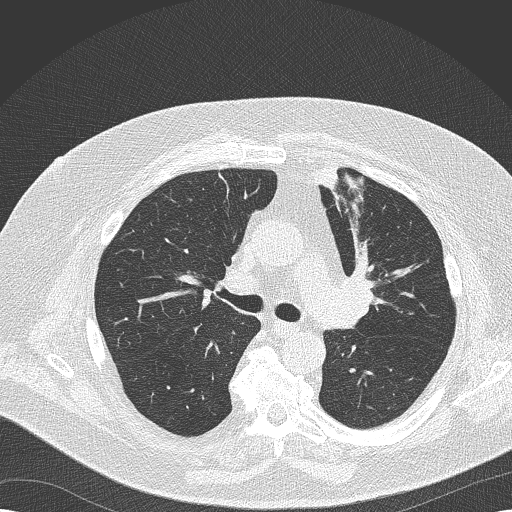
Axial slice from a low-dose chest CT screening exam, second annual screen, lung window (W 1500 / L -600 HU), 2 mm slice thickness, 512 × 512 image matrix. Male, age 68 years at enrolment. Former smoker at enrolment.
• Expert reader's lesion annotation, bounding box <322,266,380,329> (left, top, right, bottom; pixels).
• Reader record for this screening exam (exam-level; its link to the box is not recorded): non-calcified nodule or mass ≥4 mm, left lower lobe, 8 × 6 mm, soft tissue attenuation, pre-existing on the prior screen: yes; interval growth: no.
• Official screen result: positive, no significant change: stable abnormalities potentially related to lung cancer, unchanged since the prior screening exam.
• Lung cancer was diagnosed 256 days after this screen: squamous cell carcinoma, NOS, left upper lobe, poorly differentiated (G3), stage IIB (AJCC 6th edition), 35 mm at pathology.